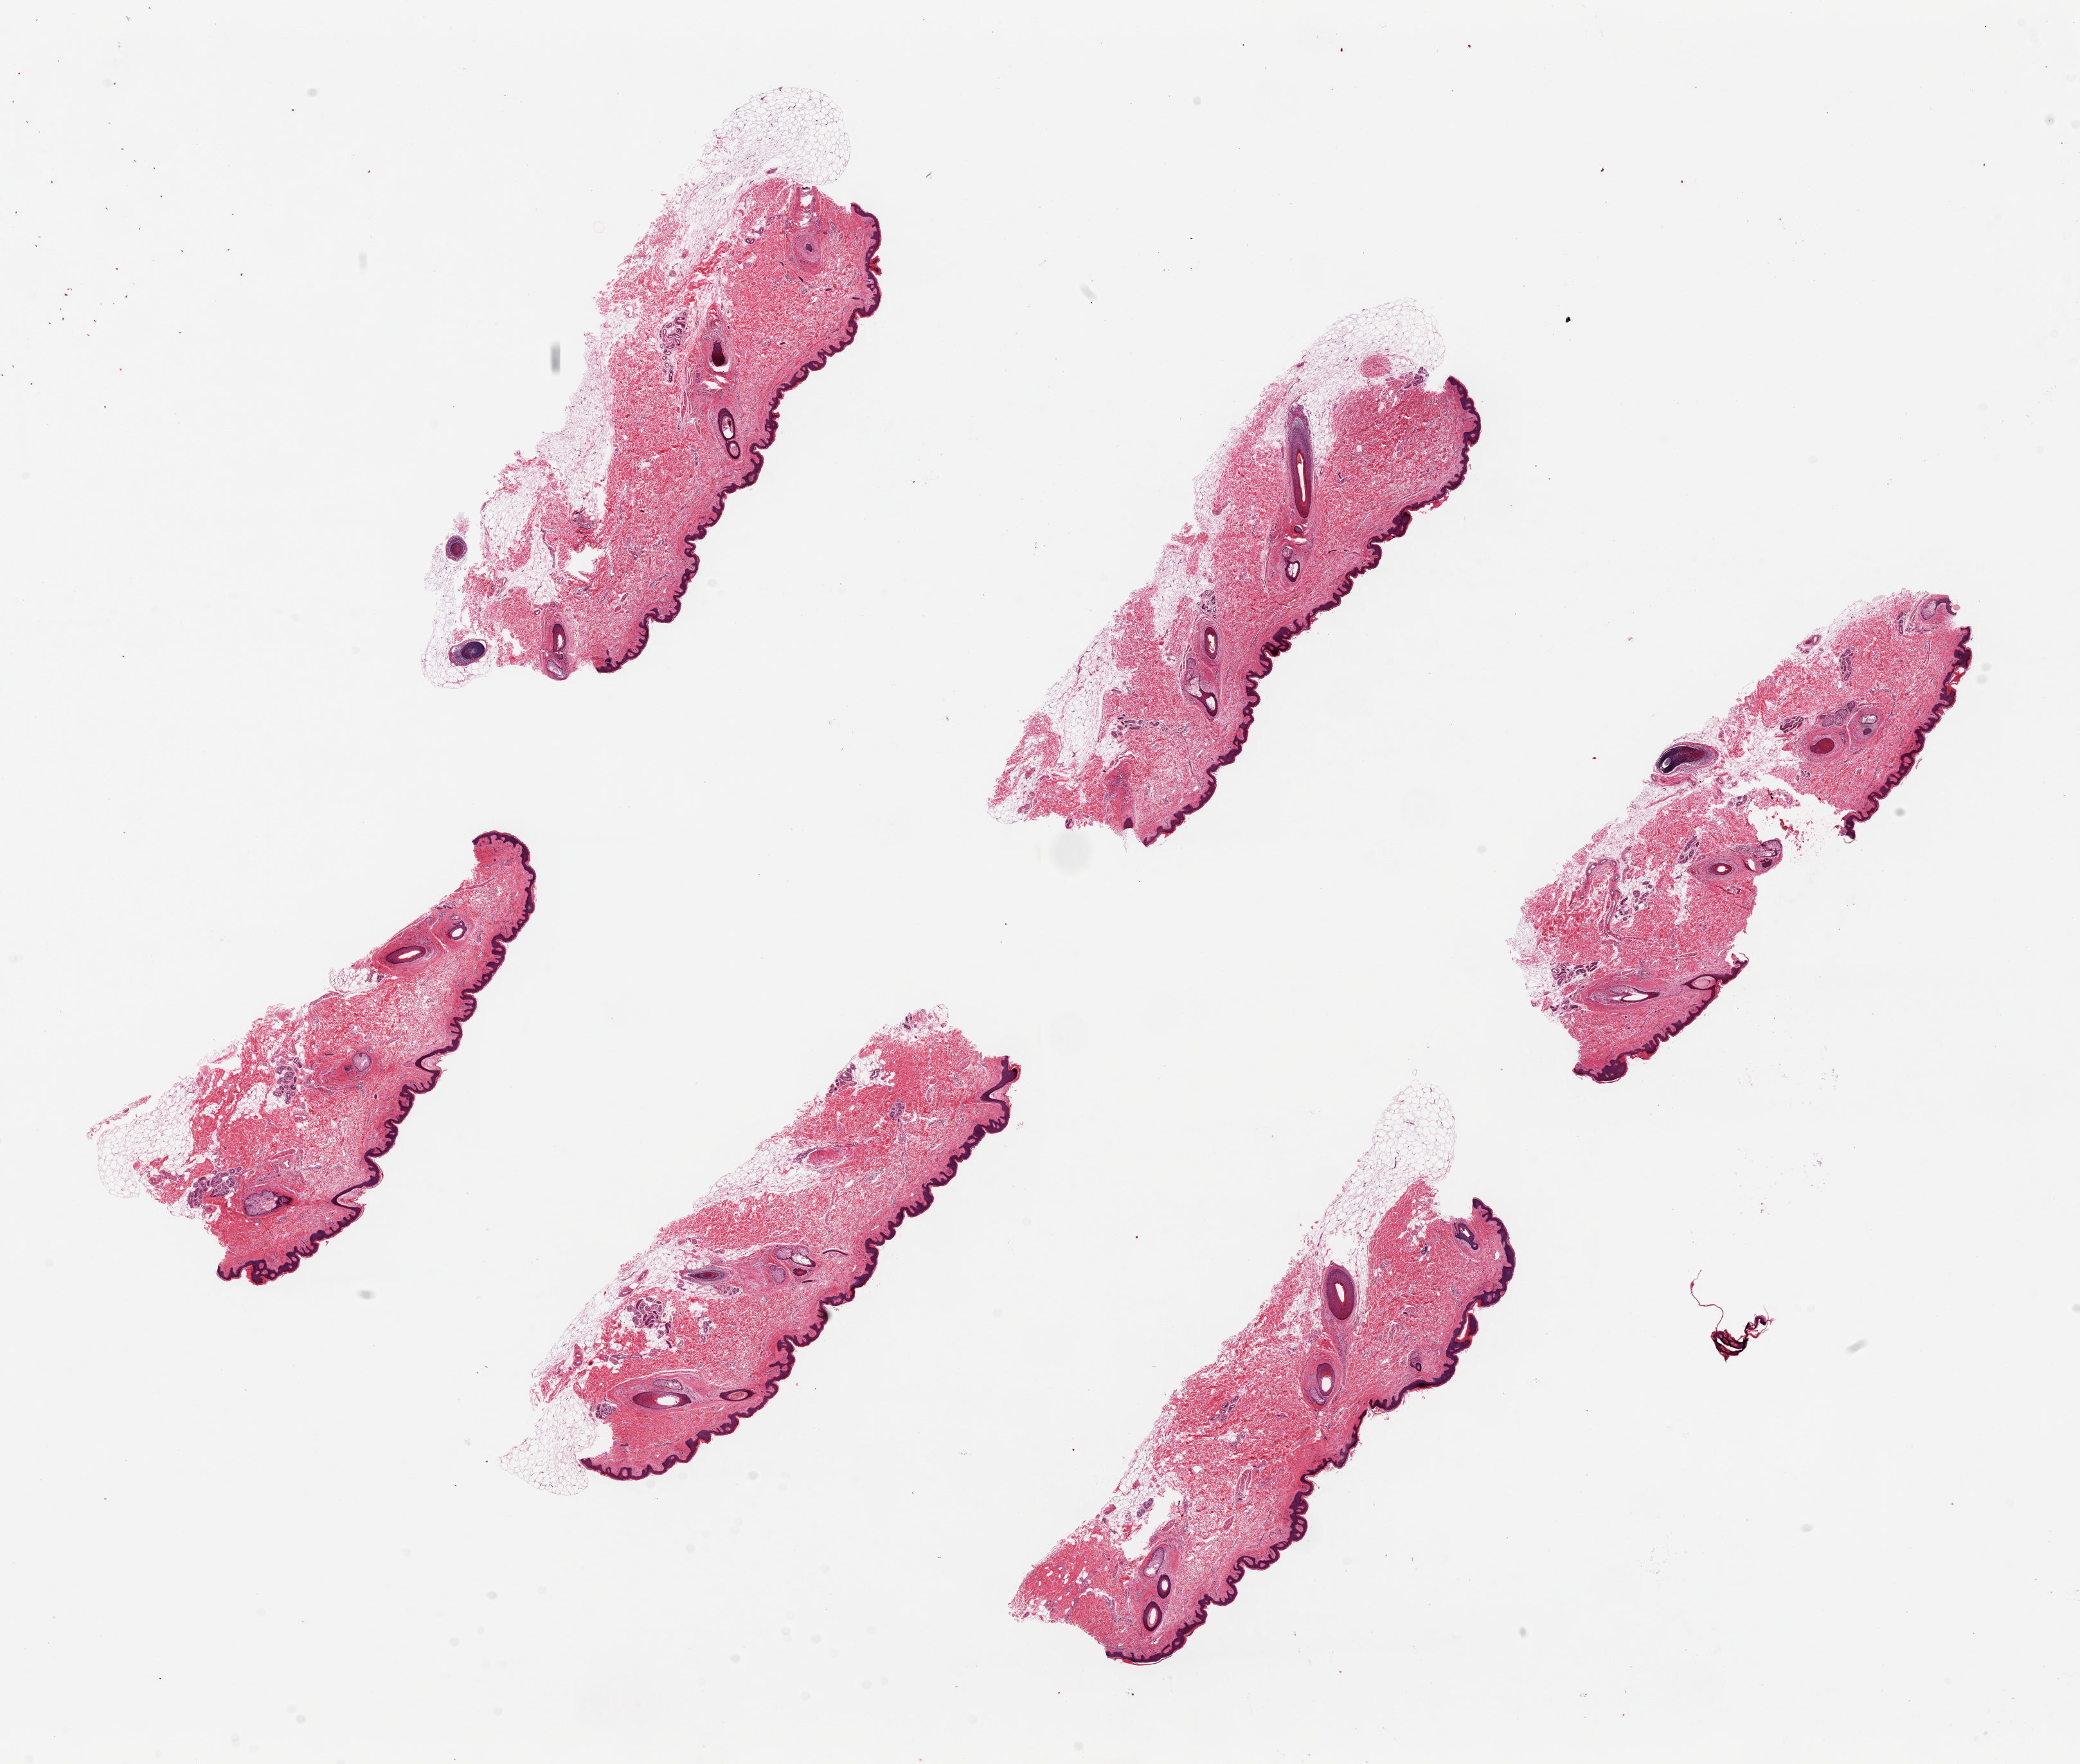
Haematoxylin and eosin whole-slide image — shown as a low-resolution overview of the whole scanned area (about 25.6 x 21.7 mm, slide scanned at 20x); PAXgene-fixed, paraffin-embedded tissue; sampled site (target tissue): skin of suprapubic region; donor tissue sample. Donor: female.
* reviewer comment on this tissue sample: 6 pieces ~7x2mm. Squamous epithelium is ~2-3.5% of thickness